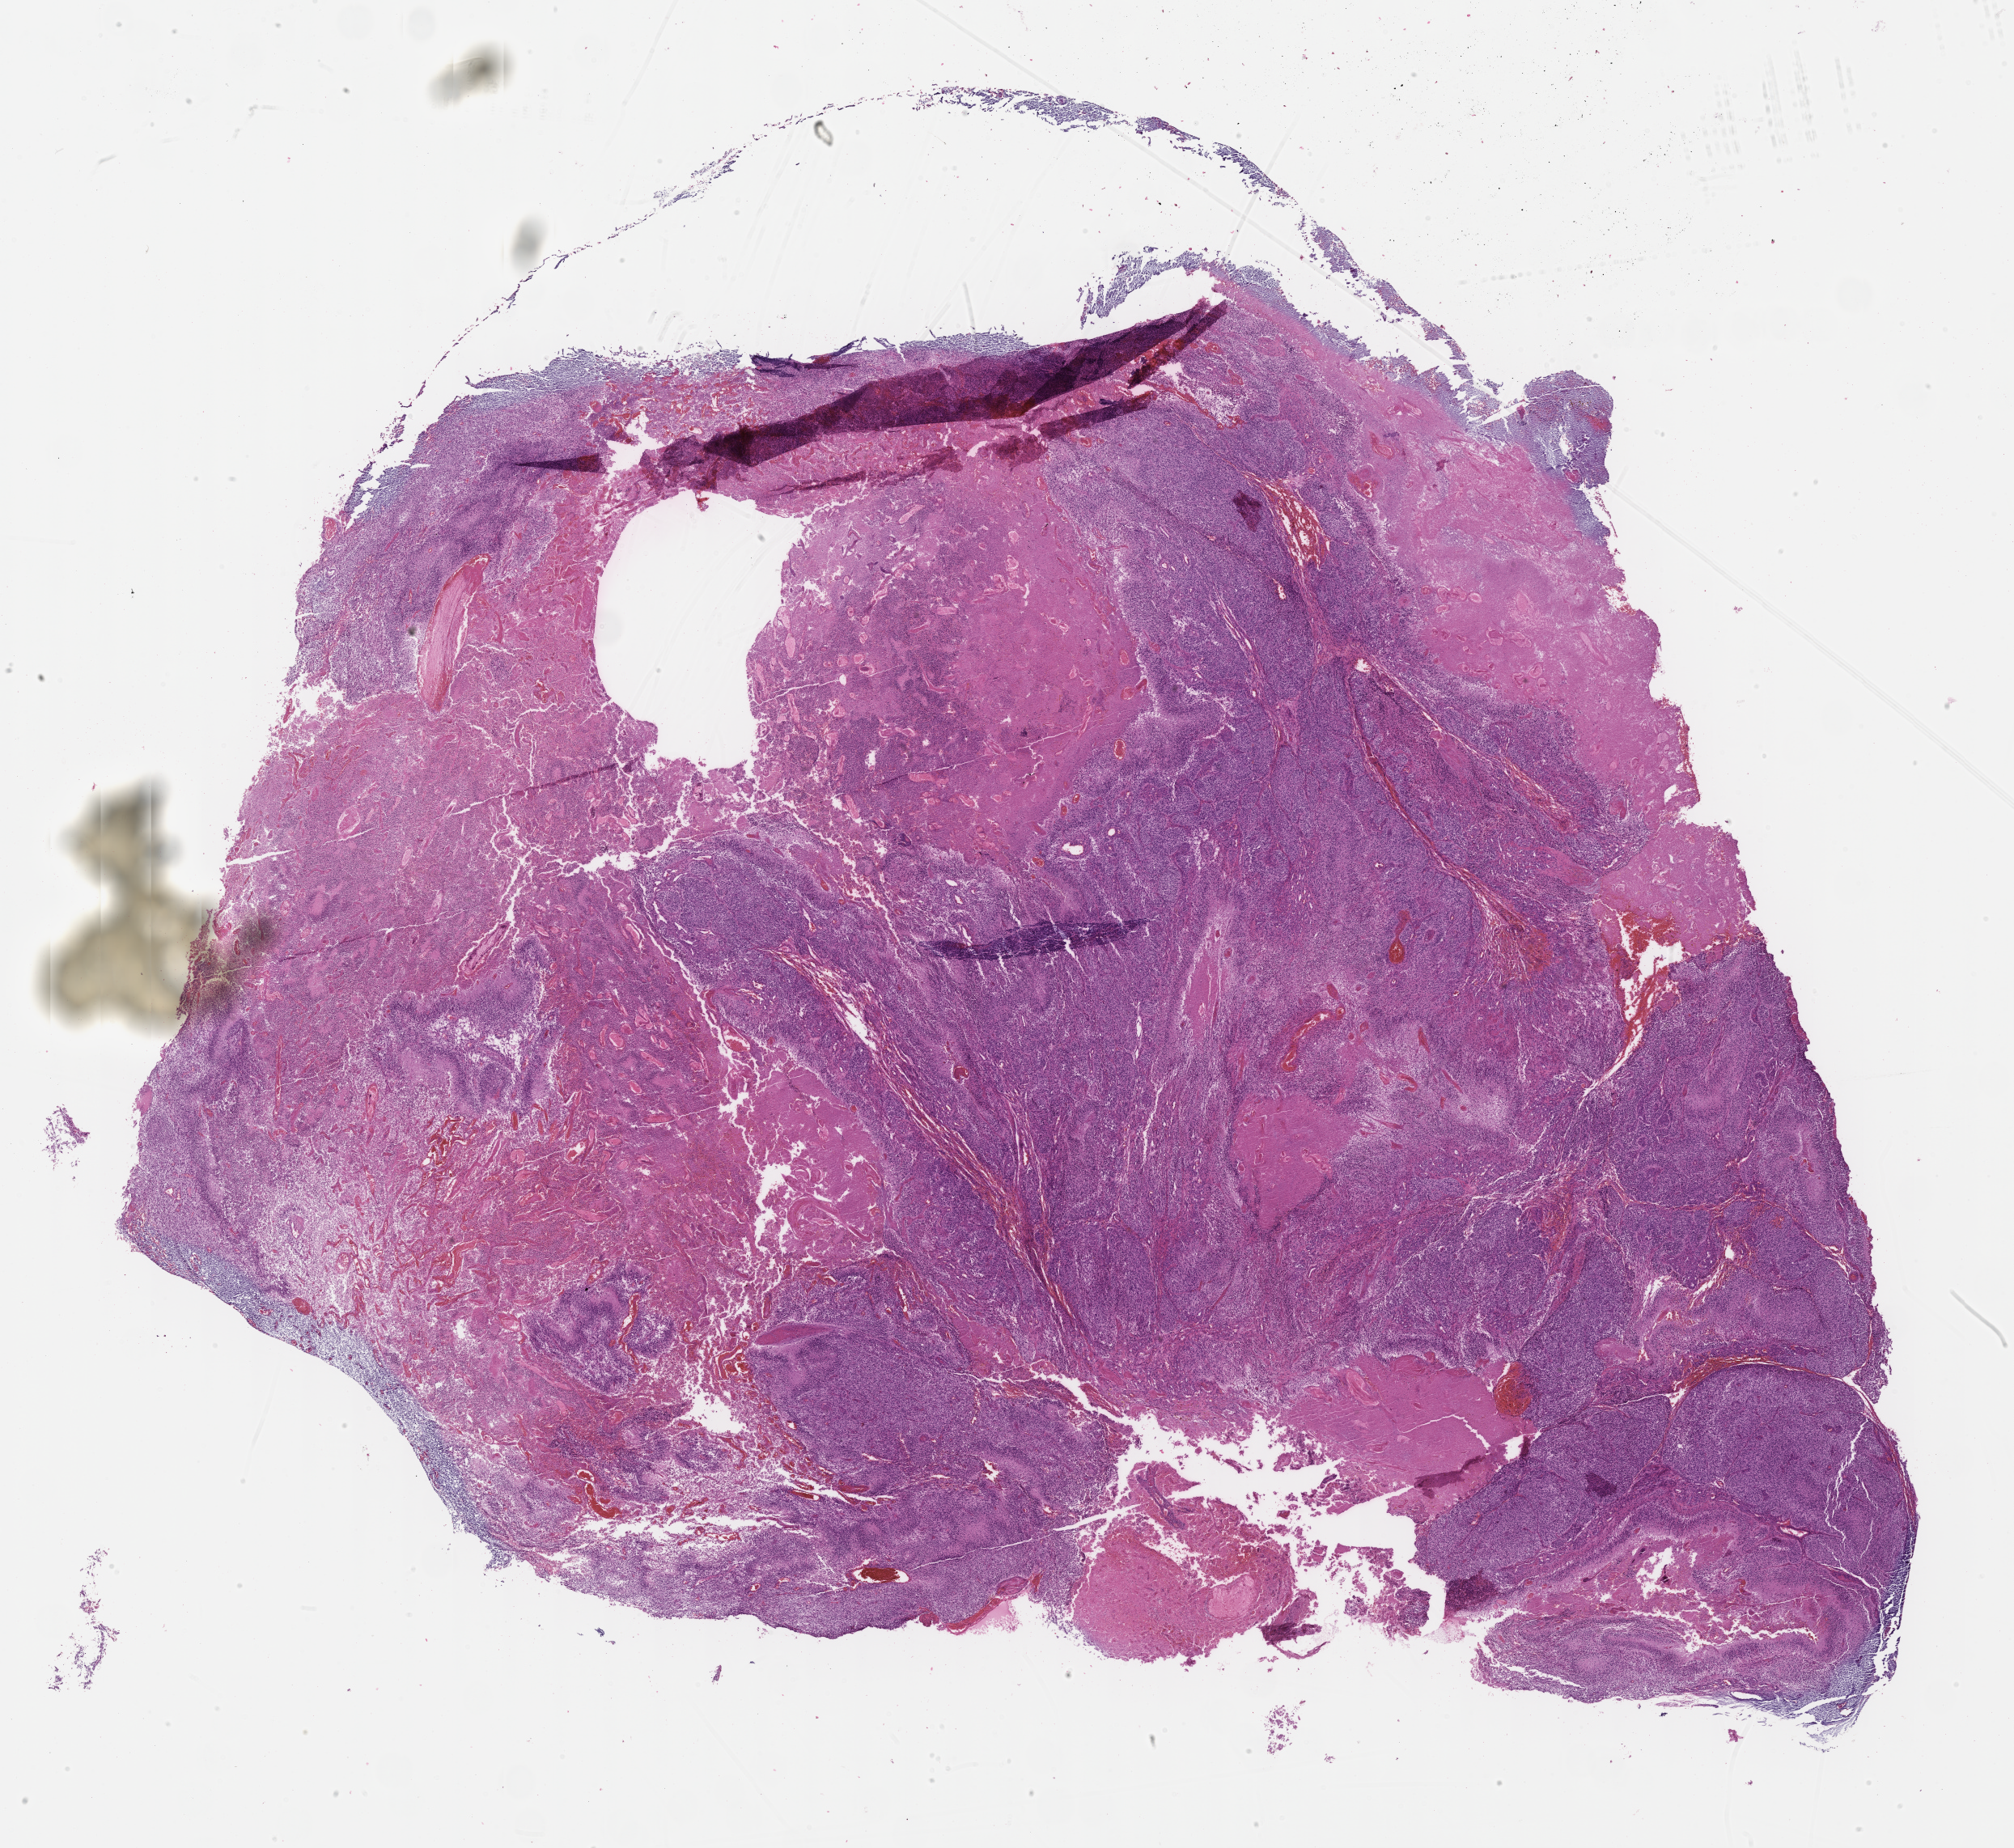
Whole-slide histology image, H&E, low-resolution overview of the scanned area, about 20.2 x 18.5 mm (from a 40x scan). FFPE section. Primary tumour sample from the brain. Patient: male, age at initial diagnosis 40 years.
- pathologic diagnosis: Glioblastoma